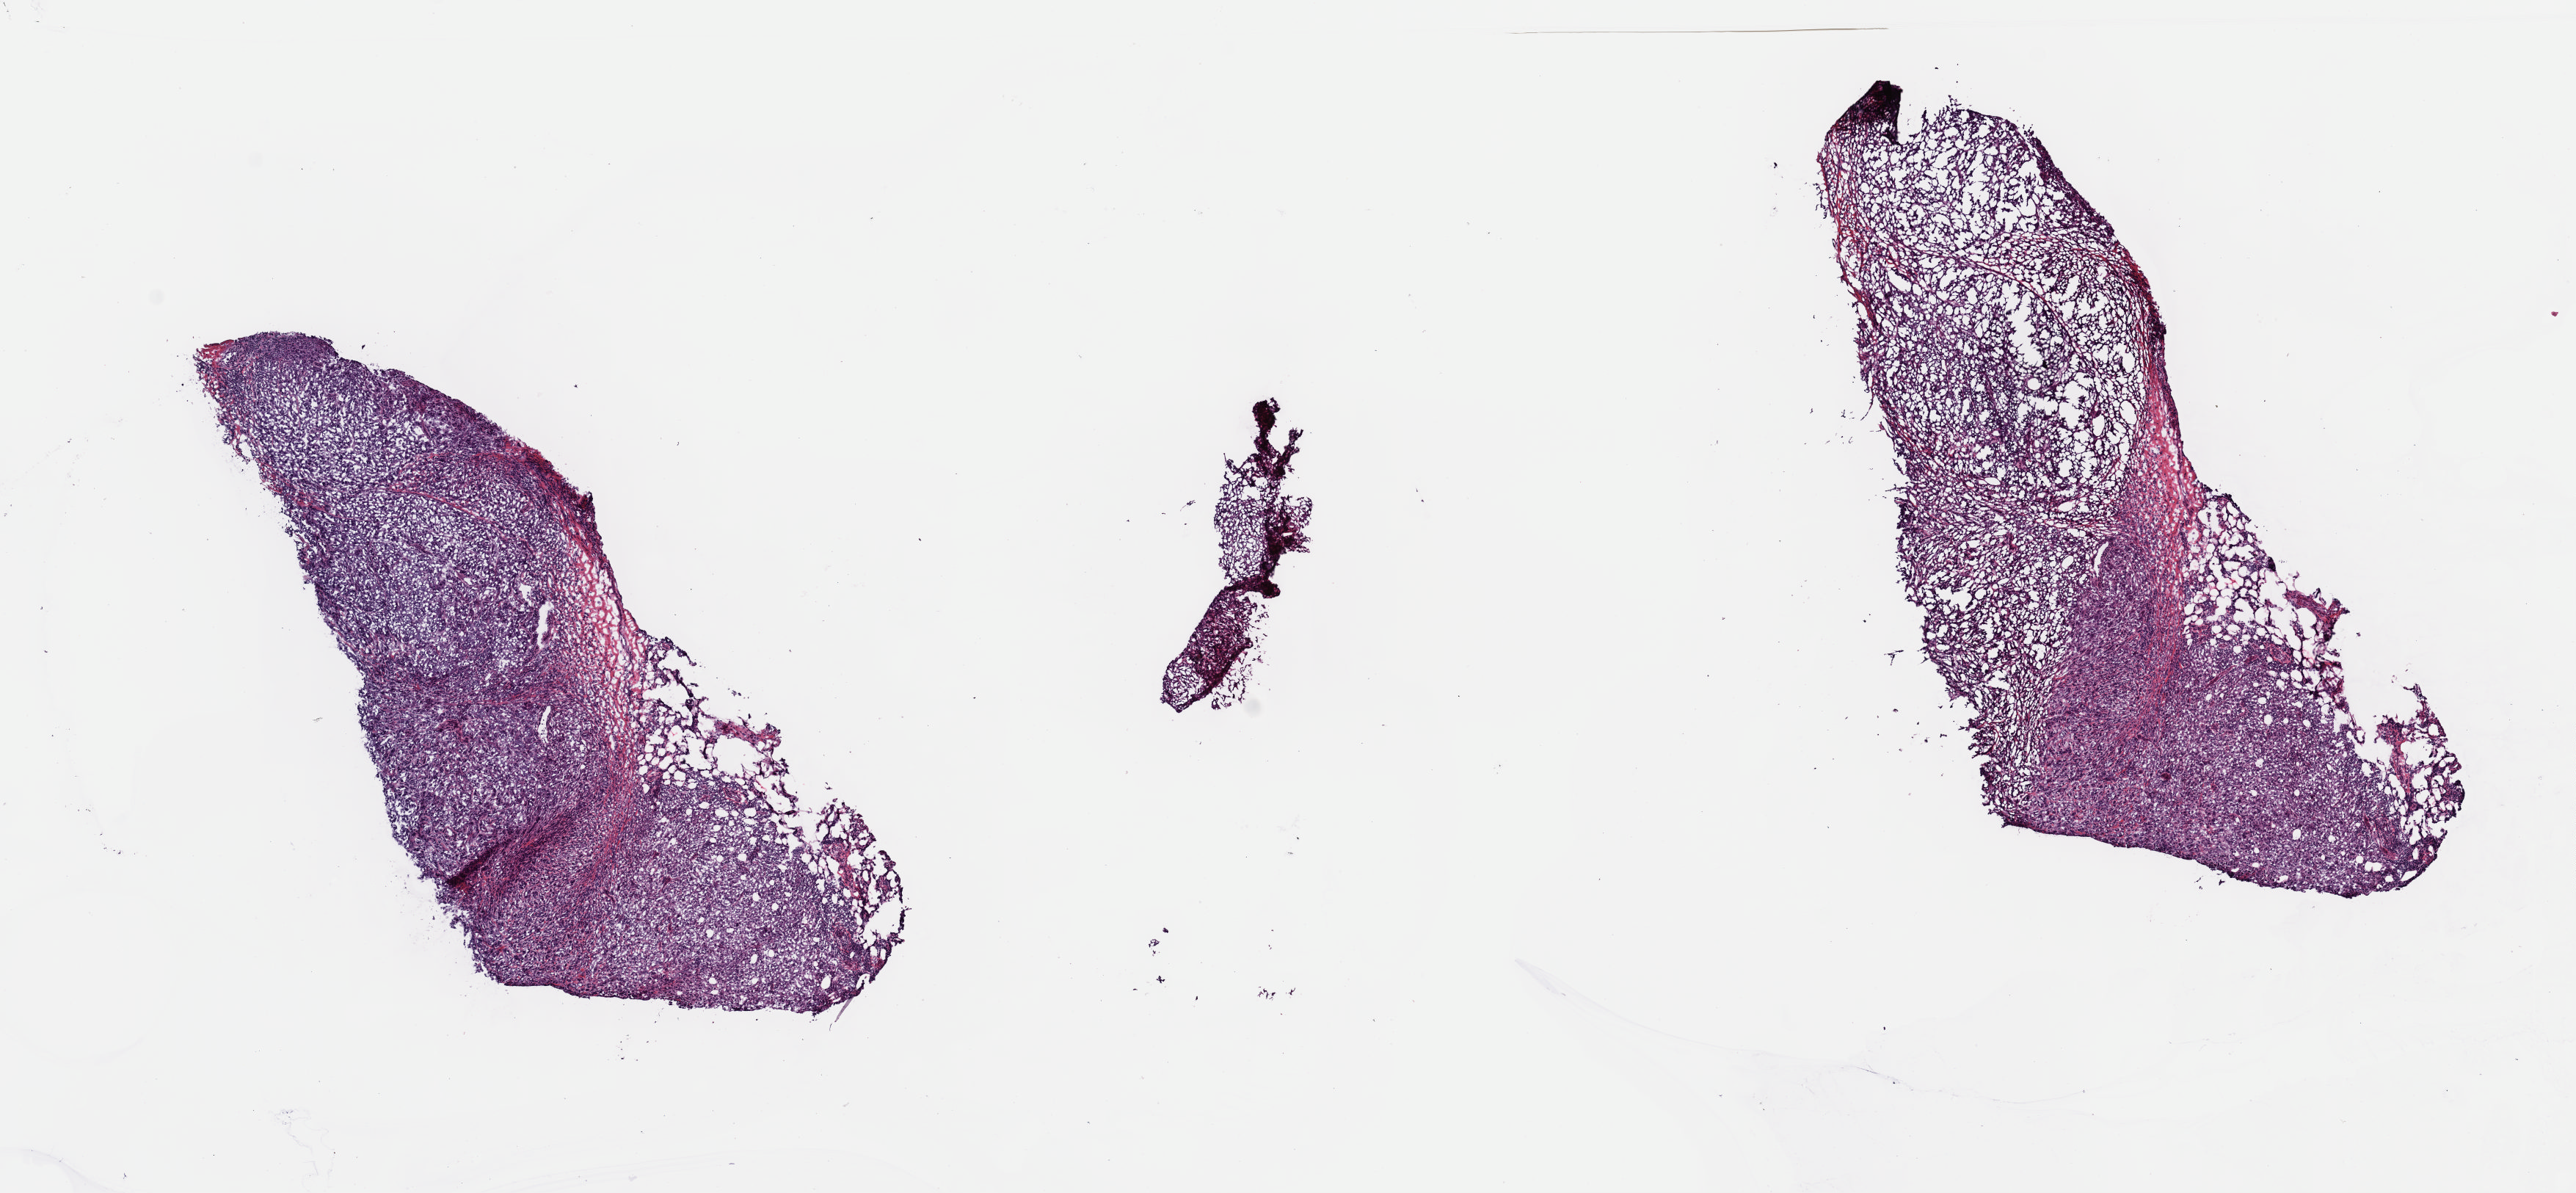
H&E whole-slide image, whole scanned area (about 13.9 x 6.4 mm) shown as a low-resolution overview, frozen section from the top of the tissue portion, metastatic tumour sample. Male, age 71 years at initial diagnosis. Composition of this section per pathologist review: tumour cells 80%, tumour nuclei 80%, normal cells 0%, stromal cells 20%, necrosis 0%. Infiltration values recorded for this section: lymphocyte infiltration 7%, monocyte infiltration 0%, neutrophil infiltration 0%.
This section: metastatic tumour tissue. Patient diagnosis: Malignant melanoma, NOS.